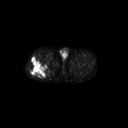
FDG PET of an extremity soft-tissue mass (from a PET/CT study), one axial slice. Slice 261 of 267 in the series (ordered by position). 3.27 mm slice thickness. 128 × 128 image matrix, field of view 700 × 700 mm. Male patient, age 43 years. From the clinical record (not read from this slice): histological type: poorly differentiated synovial sarcoma; grade: high; site of the primary tumour: right buttock.
Structures marked on this image (expert contour drawn on MRI and transferred to this co-registered scan by the dataset authors):
- gross tumour volume including surrounding oedema: box from (x=27, y=57) to (x=50, y=78) px
- gross tumour volume (mass): (x=27, y=57)–(x=48, y=78)